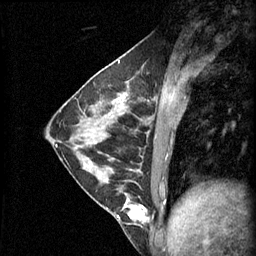
Breast MRI (dynamic contrast-enhanced), one sagittal slice; slice 22 of 60 in the series (ordered by position); 3 images stored at this slice position (order not interpretable as contrast timing); 1.5 T; TE 4.2 ms, TR 11 ms; 2.1 mm slice thickness; 256 × 256 image matrix, field of view 180 × 180 mm. Female patient, age 29 years.
Structures marked on this image (semi-automatic segmentation, software-assisted and operator-edited):
- analysis volume of interest (the breast-tissue region the enhancement analysis was run in; not a lesion): box from (x=93, y=164) to (x=153, y=225) px
- tumour enhancement mask (voxels above the 70 % enhancement threshold inside the analysis volume of interest): (x=117, y=170)–(x=149, y=223)